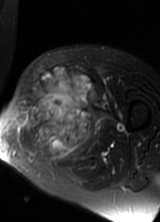
MRI of an extremity soft-tissue mass, one axial slice. Slice 40 of 69 in the series (ordered by position). T2-weighted fat-saturated. MR volume resampled by the dataset authors to the PET/CT grid (not the native acquisition matrix). 3.27 mm slice thickness. 160 × 222 image matrix, field of view 156 × 217 mm. Female patient. From the clinical record (not read from this slice): histological type: pleomorphic leiomyosarcoma; grade: high; site of the primary tumour: left thigh.
Annotated regions visible in this slice (expert contour drawn on MRI and transferred to this co-registered scan by the dataset authors):
- gross tumour volume including surrounding oedema: bounding box [x1, y1, x2, y2] px = [20, 68, 96, 162]
- gross tumour volume (mass): [27, 68, 96, 151]